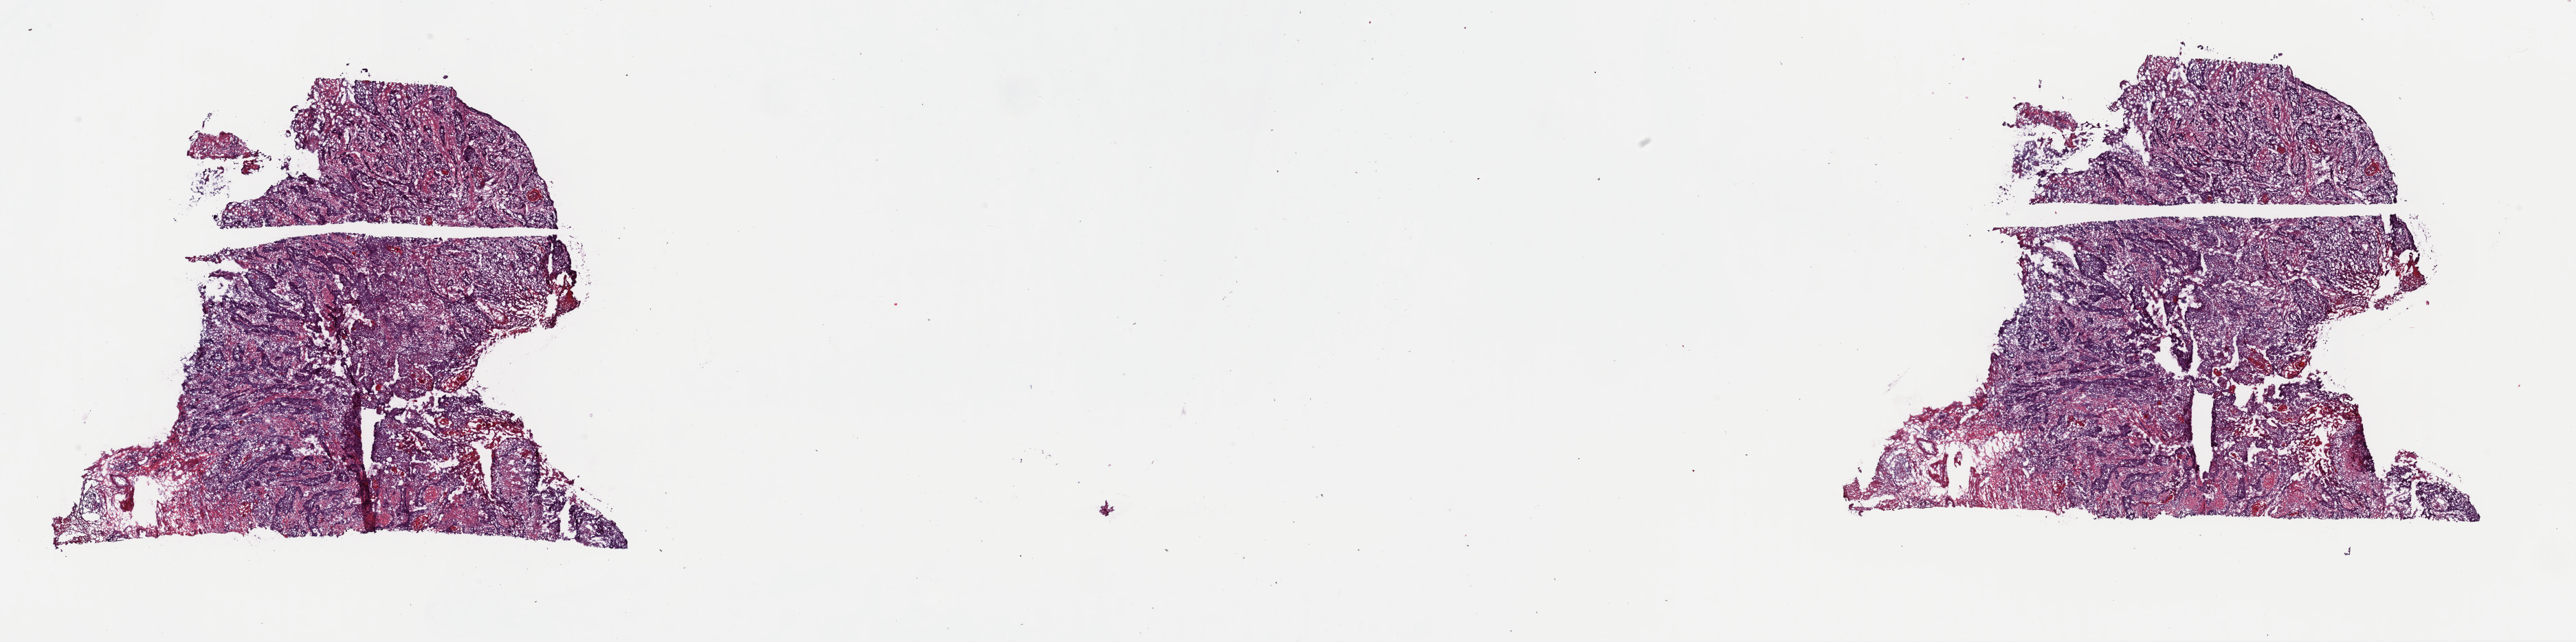
Whole-slide histology image, H&E, shown as a low-resolution overview of the whole scanned area (about 29.6 x 7.4 mm, from a 40x scan). Frozen section from the top of the tissue portion. Primary tumour sample from the esophagus. Male, age 44 years at initial diagnosis. Histologic grade: G2 (moderately differentiated). Slide review estimates, as recorded: tumour cells 70%, tumour nuclei 70%, normal cells 0%, stromal cells 30%, necrosis 0%. Infiltration values recorded for this section: lymphocyte infiltration 2%, monocyte infiltration 0%, neutrophil infiltration 0%.
- histologic diagnosis: Squamous cell carcinoma, NOS (middle third of esophagus)
- AJCC pathologic stage: IIA (6th edition)